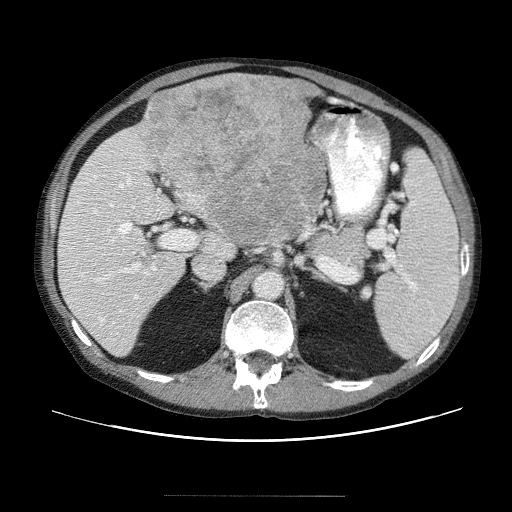
Contrast-enhanced abdominal CT (liver protocol), one axial slice. Slice 25 of 69 in the series (ordered by position). 120 kVp. Soft-tissue window (W 400 / L 40 HU). 2.5 mm slice thickness. 512 × 512 image matrix, field of view 380 × 380 mm. Case-level facts recorded for this patient, not image findings: diagnosis: hepatocellular carcinoma (patient treated with transarterial chemoembolisation; whether this scan precedes or follows treatment is not stated here); TNM stage (as recorded): Stage-IVB; Child-Pugh class: B; tumour differentiation: poorly differentiated; tumour nodularity: multinodular.
Structures marked on this image (semi-automatically segmented with operator editing):
- liver parenchyma outside the tumour (the mass and vessels are separate outlines, so this box may not span the whole liver): bounding box [x1, y1, x2, y2] px = [56, 76, 326, 354]
- mass: [135, 76, 328, 246]
- liver vessels: [60, 166, 174, 346]